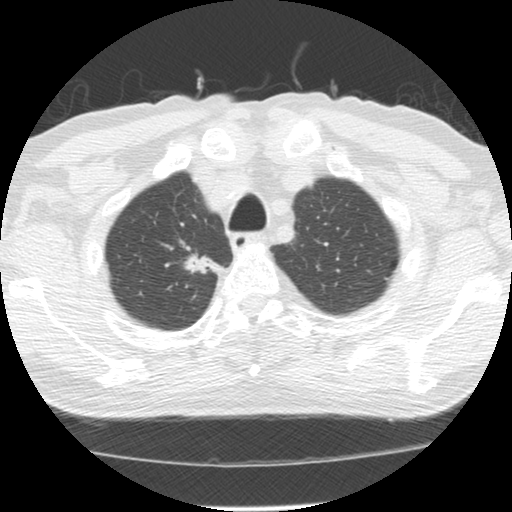
Low-dose screening chest CT, one axial slice. Position 114 of 139 along the scan axis. Reconstruction kernel STANDARD. 120 kVp. Lung window (W 1500 / L -600 HU). 2.5 mm slice thickness. 512 × 512 image matrix, field of view 310 × 310 mm.
Annotated regions visible in this slice (expert manual segmentation):
- lesion 1 (tumor, upper lobe of right lung): bounding box [x1, y1, x2, y2] px = [183, 253, 224, 275]